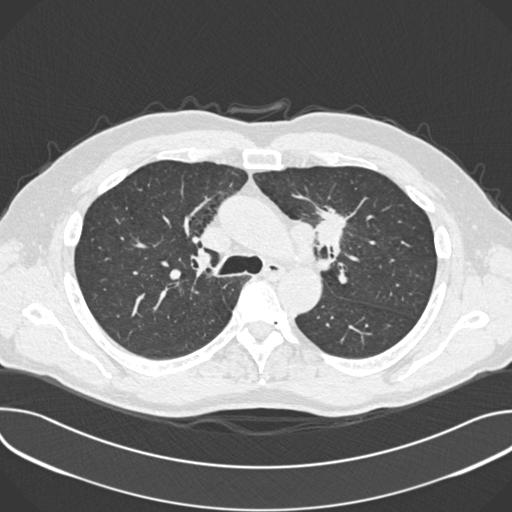
Low-dose screening chest CT, one axial slice. Slice 255 of 361 in the series (ordered by position). 120 kVp. Lung window (W 1500 / L -600 HU). 1 mm slice thickness. 512 × 512 image matrix, field of view 380 × 380 mm.
Annotated regions visible in this slice (manually delineated by an expert):
- lesion 1 (tumor, upper lobe of left lung): box from (x=316, y=207) to (x=348, y=248) px